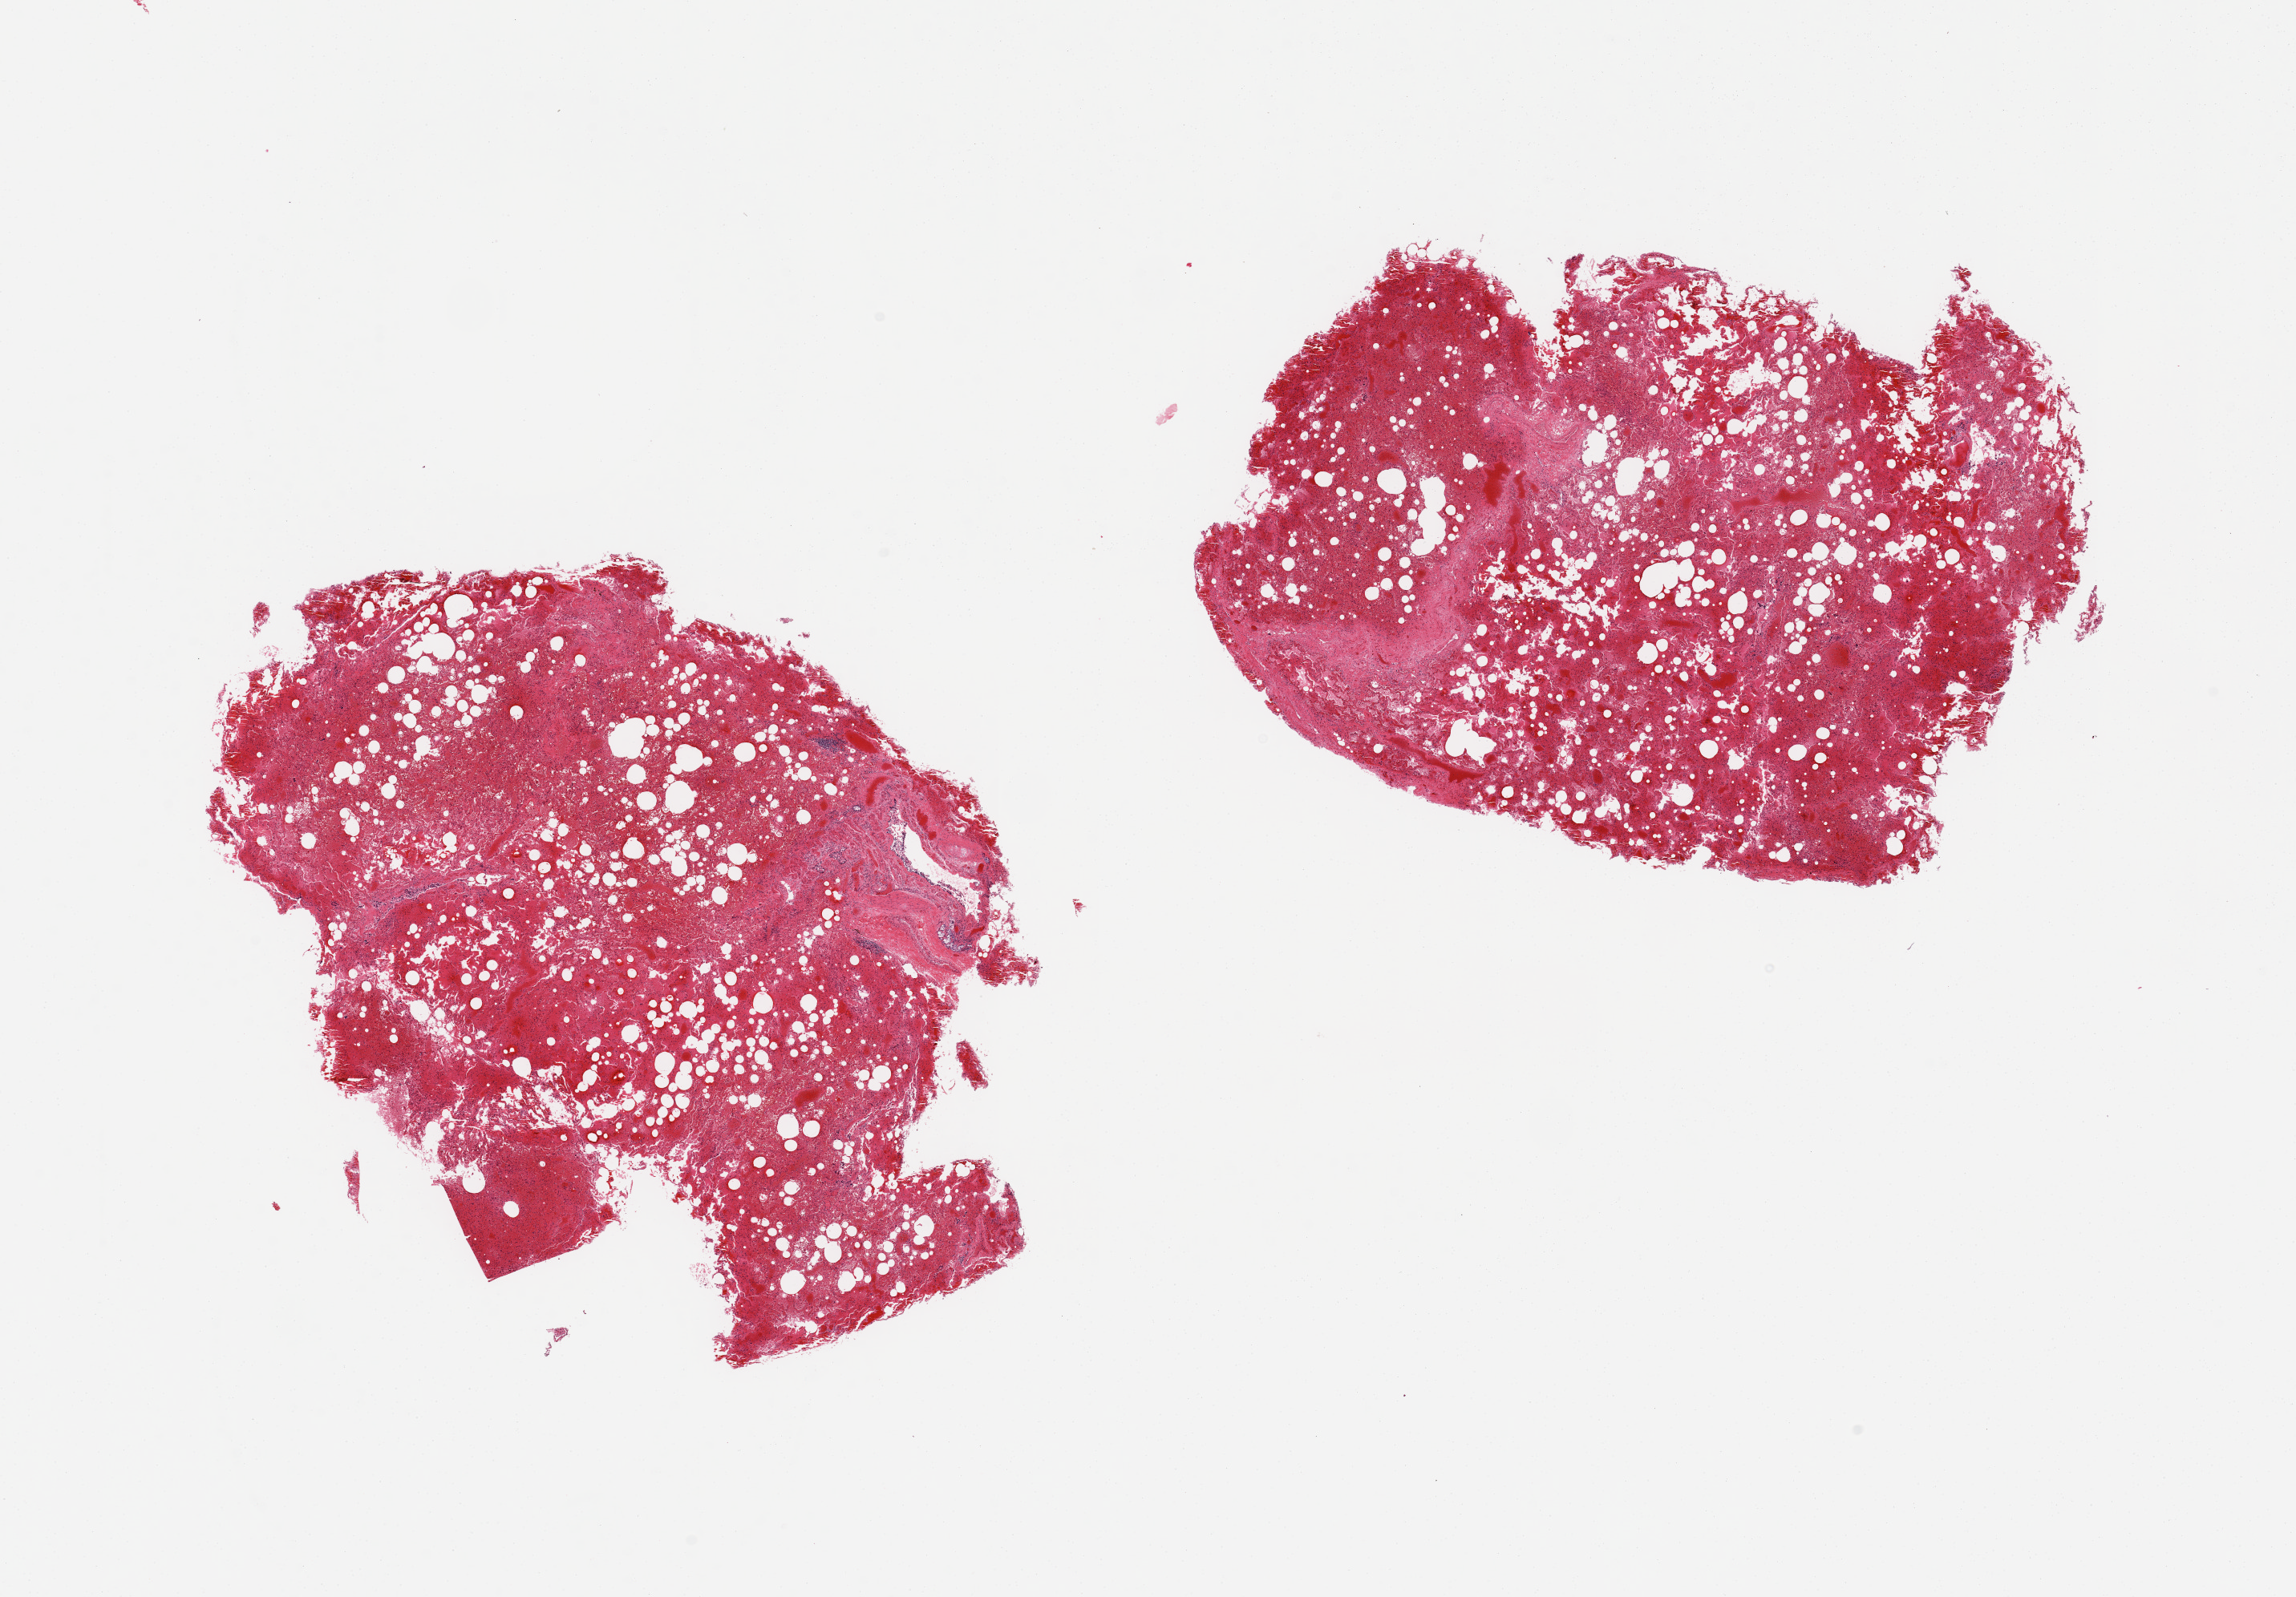
Whole-slide image, hematoxylin and eosin (H&E) stain, brightfield — shown as a low-resolution overview of the whole scanned area (about 22.6 x 15.8 mm), PAXgene-fixed, paraffin-embedded tissue, sampled site (target tissue): lung, donor tissue sample. Donor: male.
Pathologist's review note for this sample: 2 pieces; marked vascular congestion and hemorrhage.